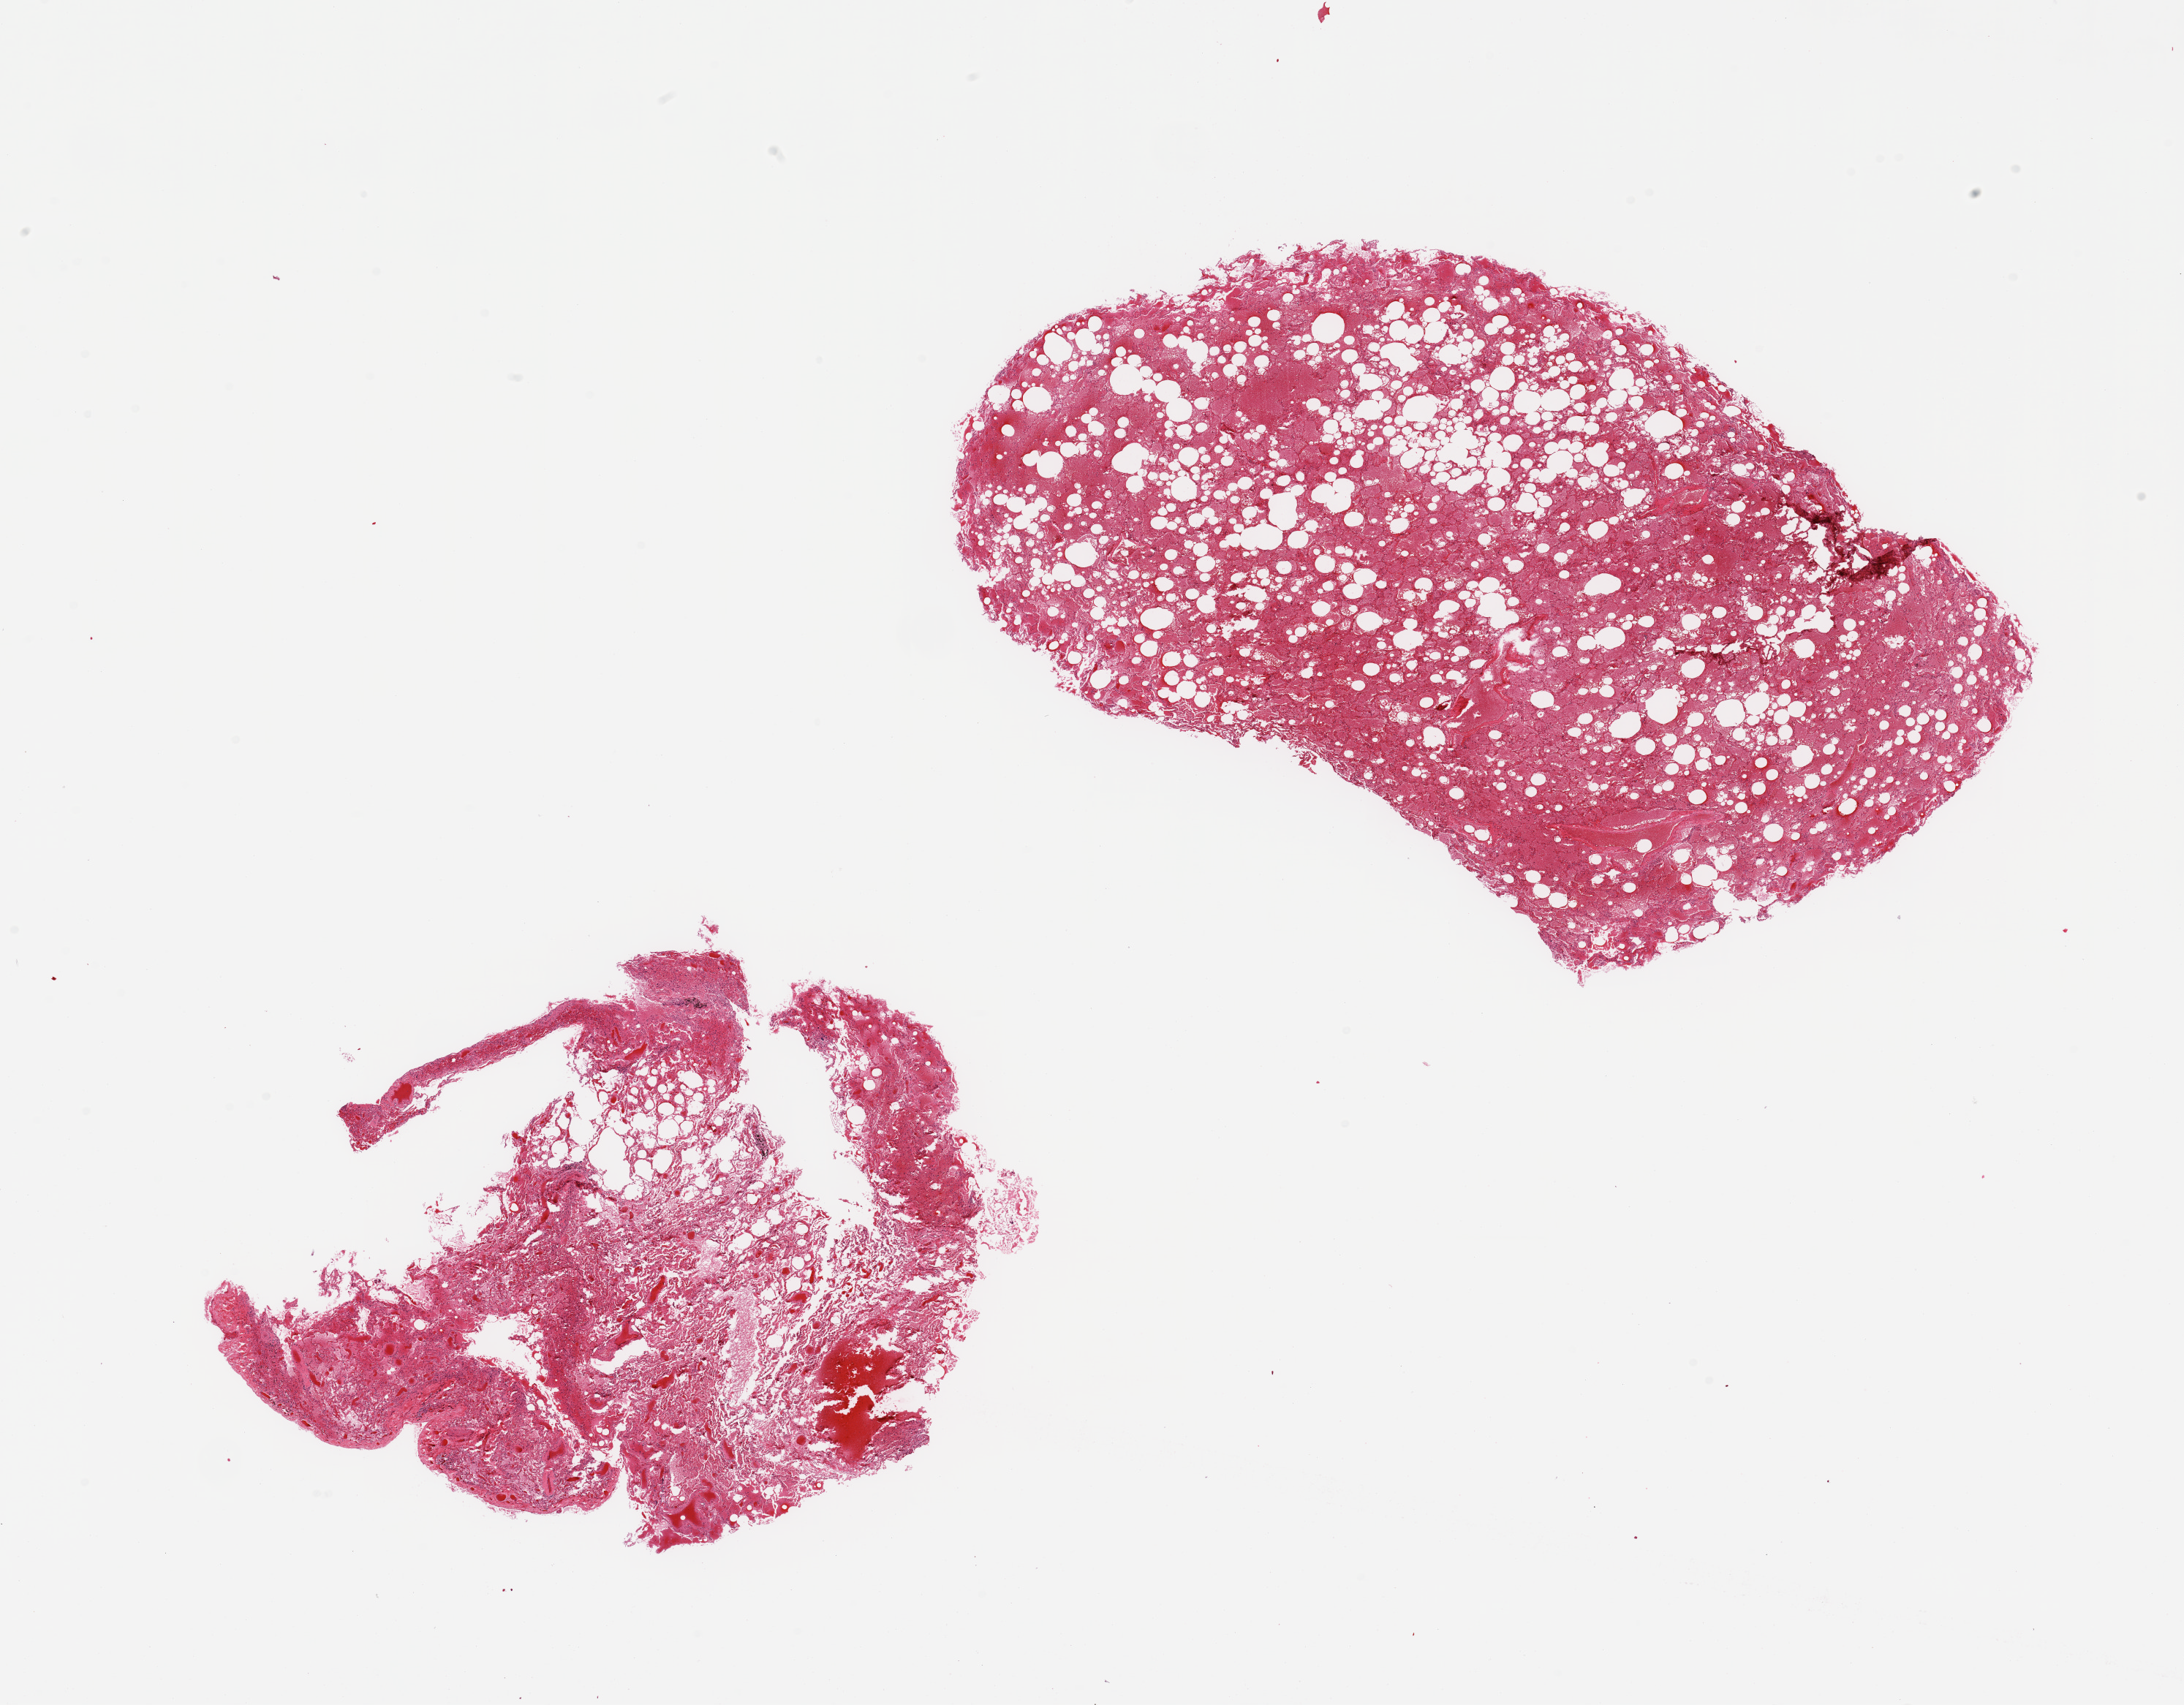
Digitized hematoxylin and eosin (H&E)-stained section, brightfield — shown as a low-resolution overview of the whole scanned area (about 23.6 x 18.4 mm, from a 20x scan), PAXgene-fixed, paraffin-embedded tissue, sampled site (target tissue): lung, tissue donor sample. Donor sex: male.
Reviewer comment on this tissue sample: 2 pieces; extensive alveolar hemorrhage; smaller piece fragmented.